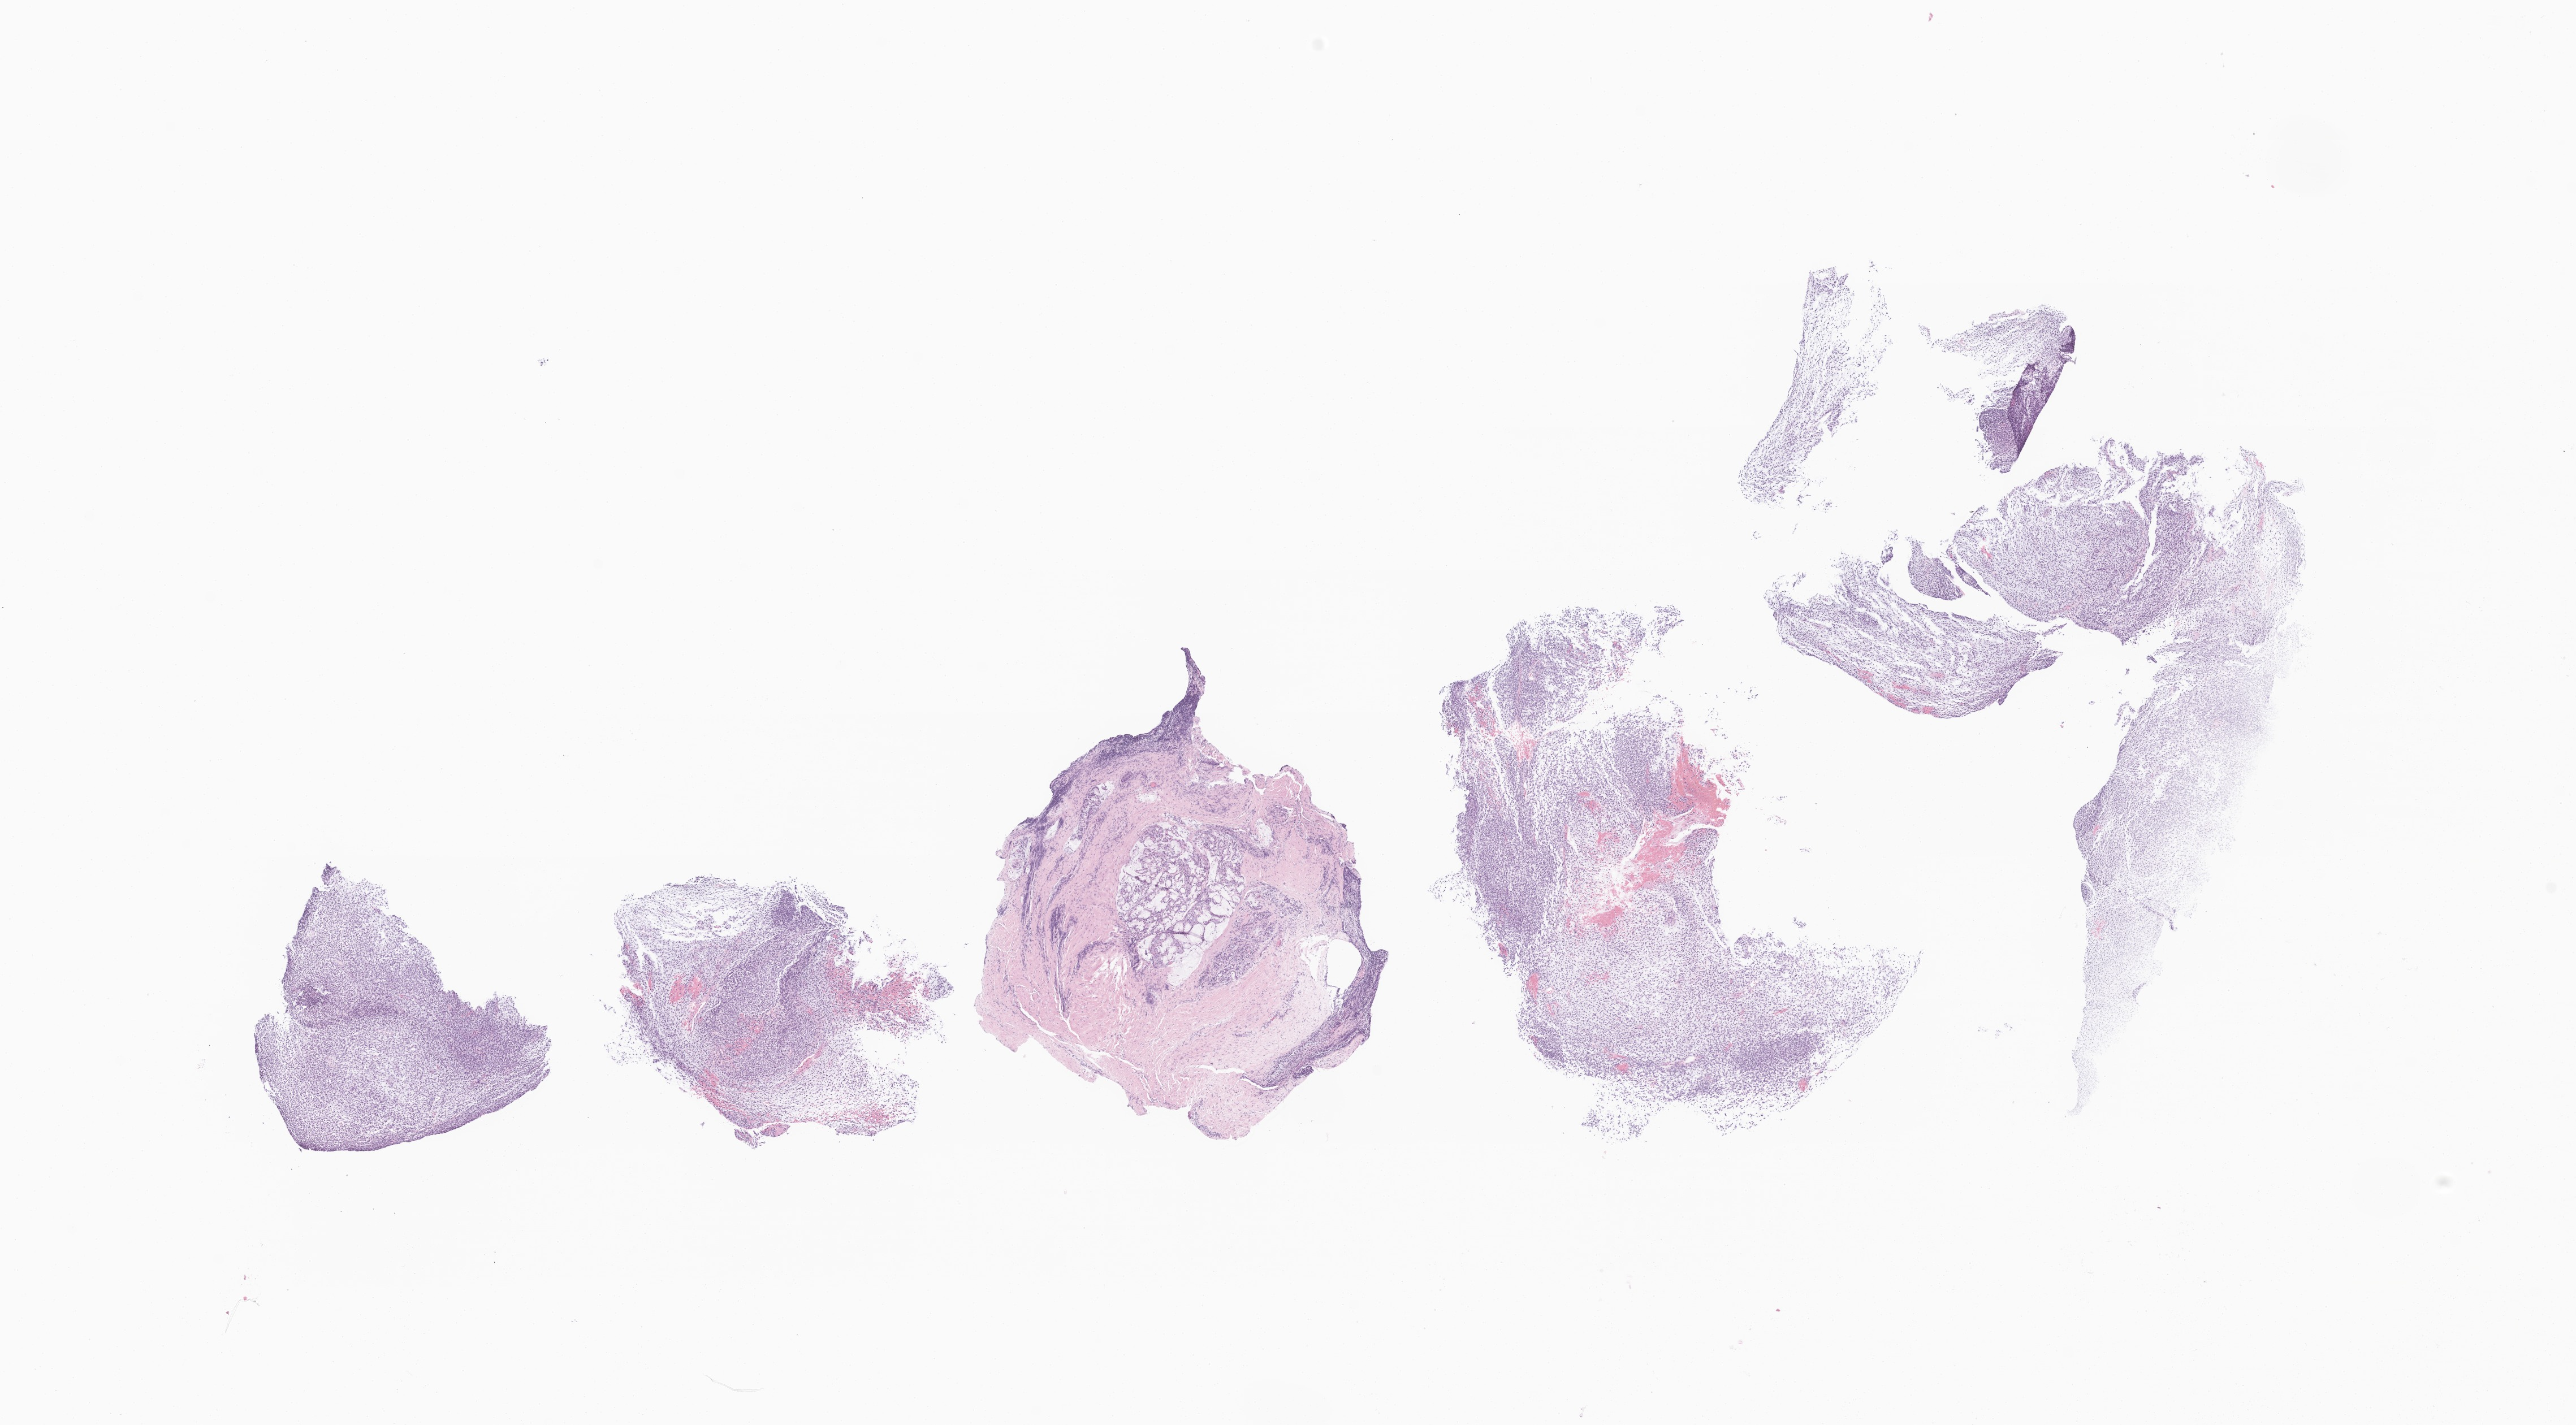
Digitized haematoxylin and eosin-stained section of tumor tissue from the nasopharynx, whole scanned area (about 19.2 x 10.6 mm) shown as a low-resolution overview, formalin-fixed, paraffin-embedded (FFPE) tissue. Patient: male, age 125 months (10 years 5 months).
• diagnosis: Rhabdomyosarcoma, NOS